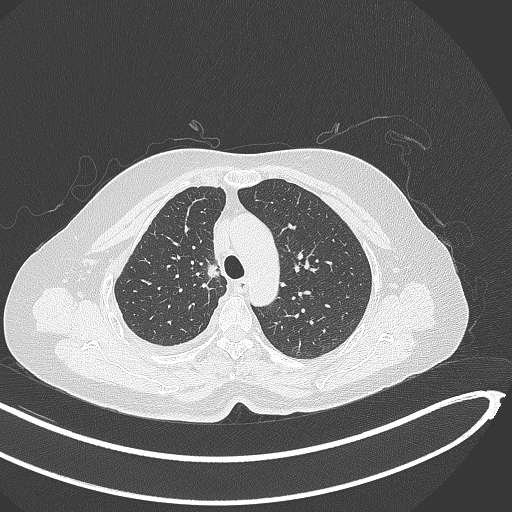
Chest CT, one axial slice. Slice 280 of 345 in the series (ordered by position). Lung window (W 1500 / L -600 HU). 512 × 512 image matrix, field of view 400 × 400 mm. Patient: female, 64 years. From the clinical record (not read from this slice): clinical TNM (as recorded): T1b N0 M1.
Annotated regions visible in this slice (bounding box drawn by a radiologist):
- lung tumour (recorded histology: adenocarcinoma): bounding box <200,257,225,284> (left, top, right, bottom; pixels)